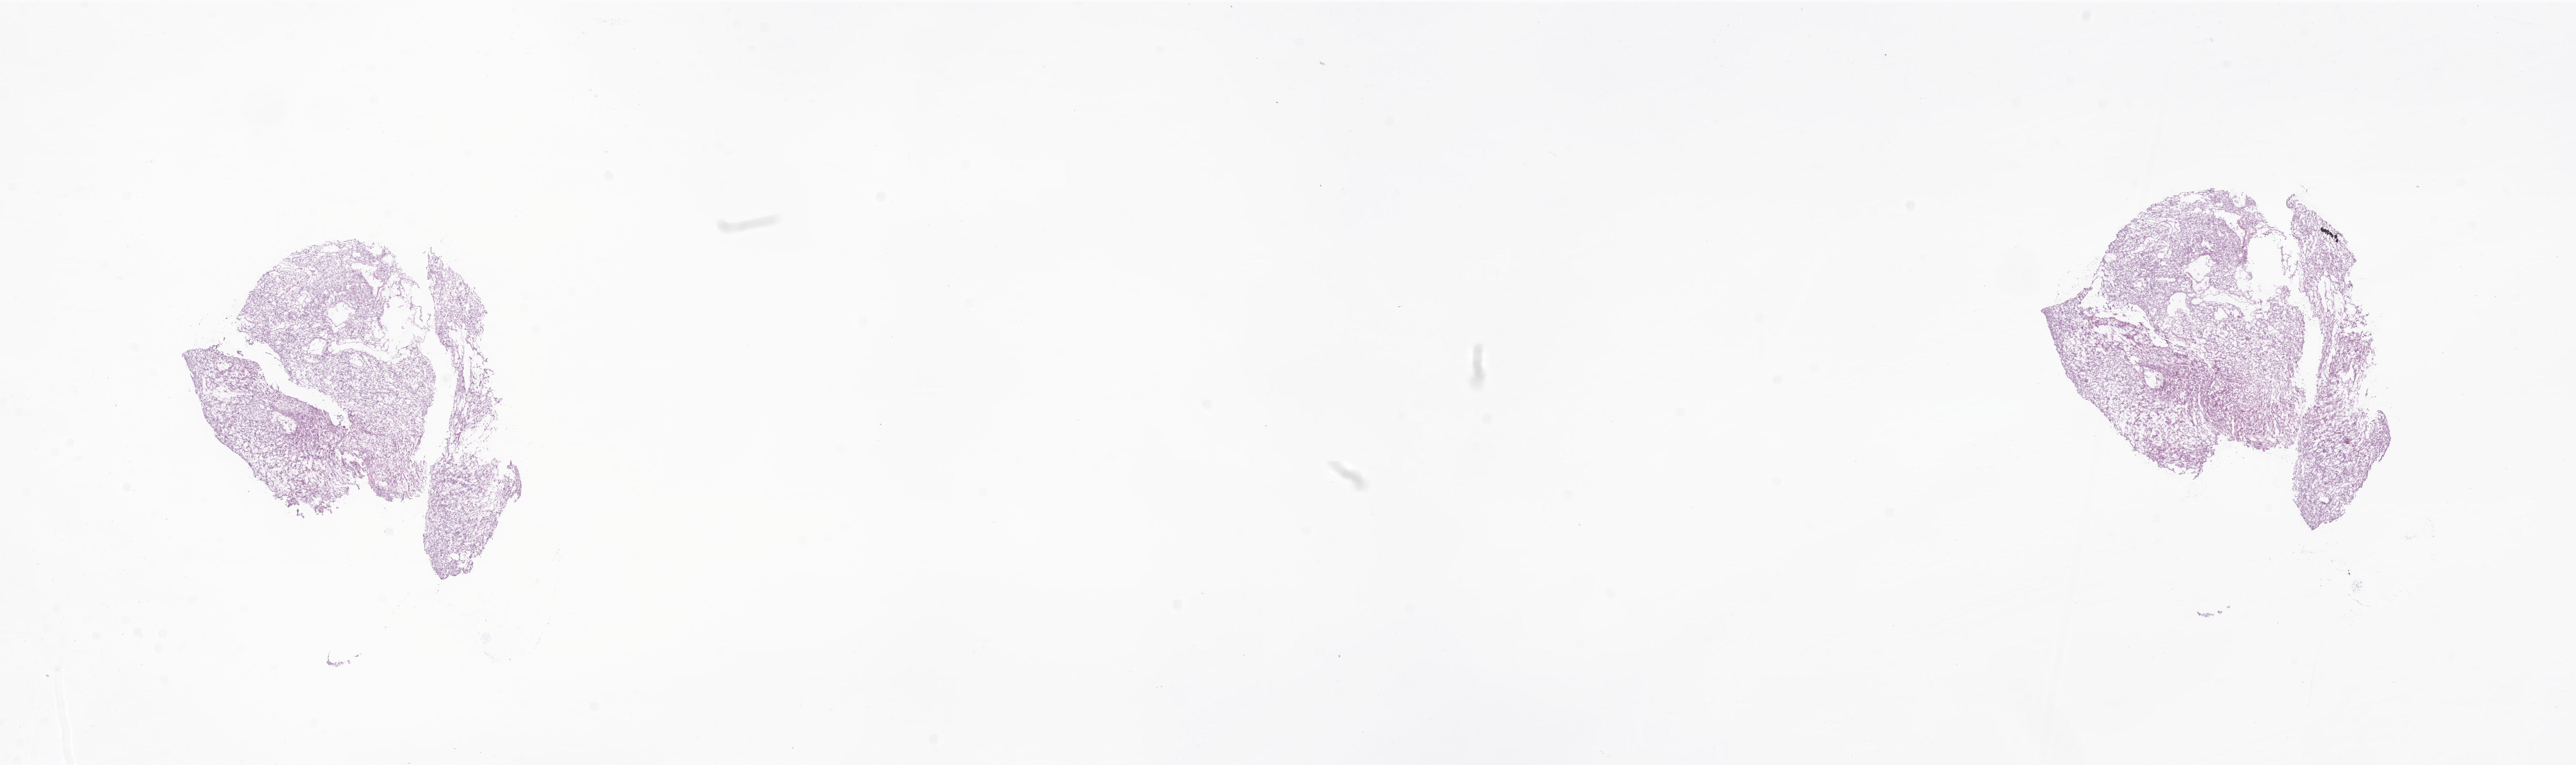
Whole-slide image, hematoxylin and eosin (H&E) stain of tumor tissue from the cerebral ventricle, a low-resolution overview of the entire scanned area, about 26.9 x 8.0 mm; cryosection (OCT / tissue freezing medium). Patient female; age 251 months.
* diagnosis: Hemangioblastoma